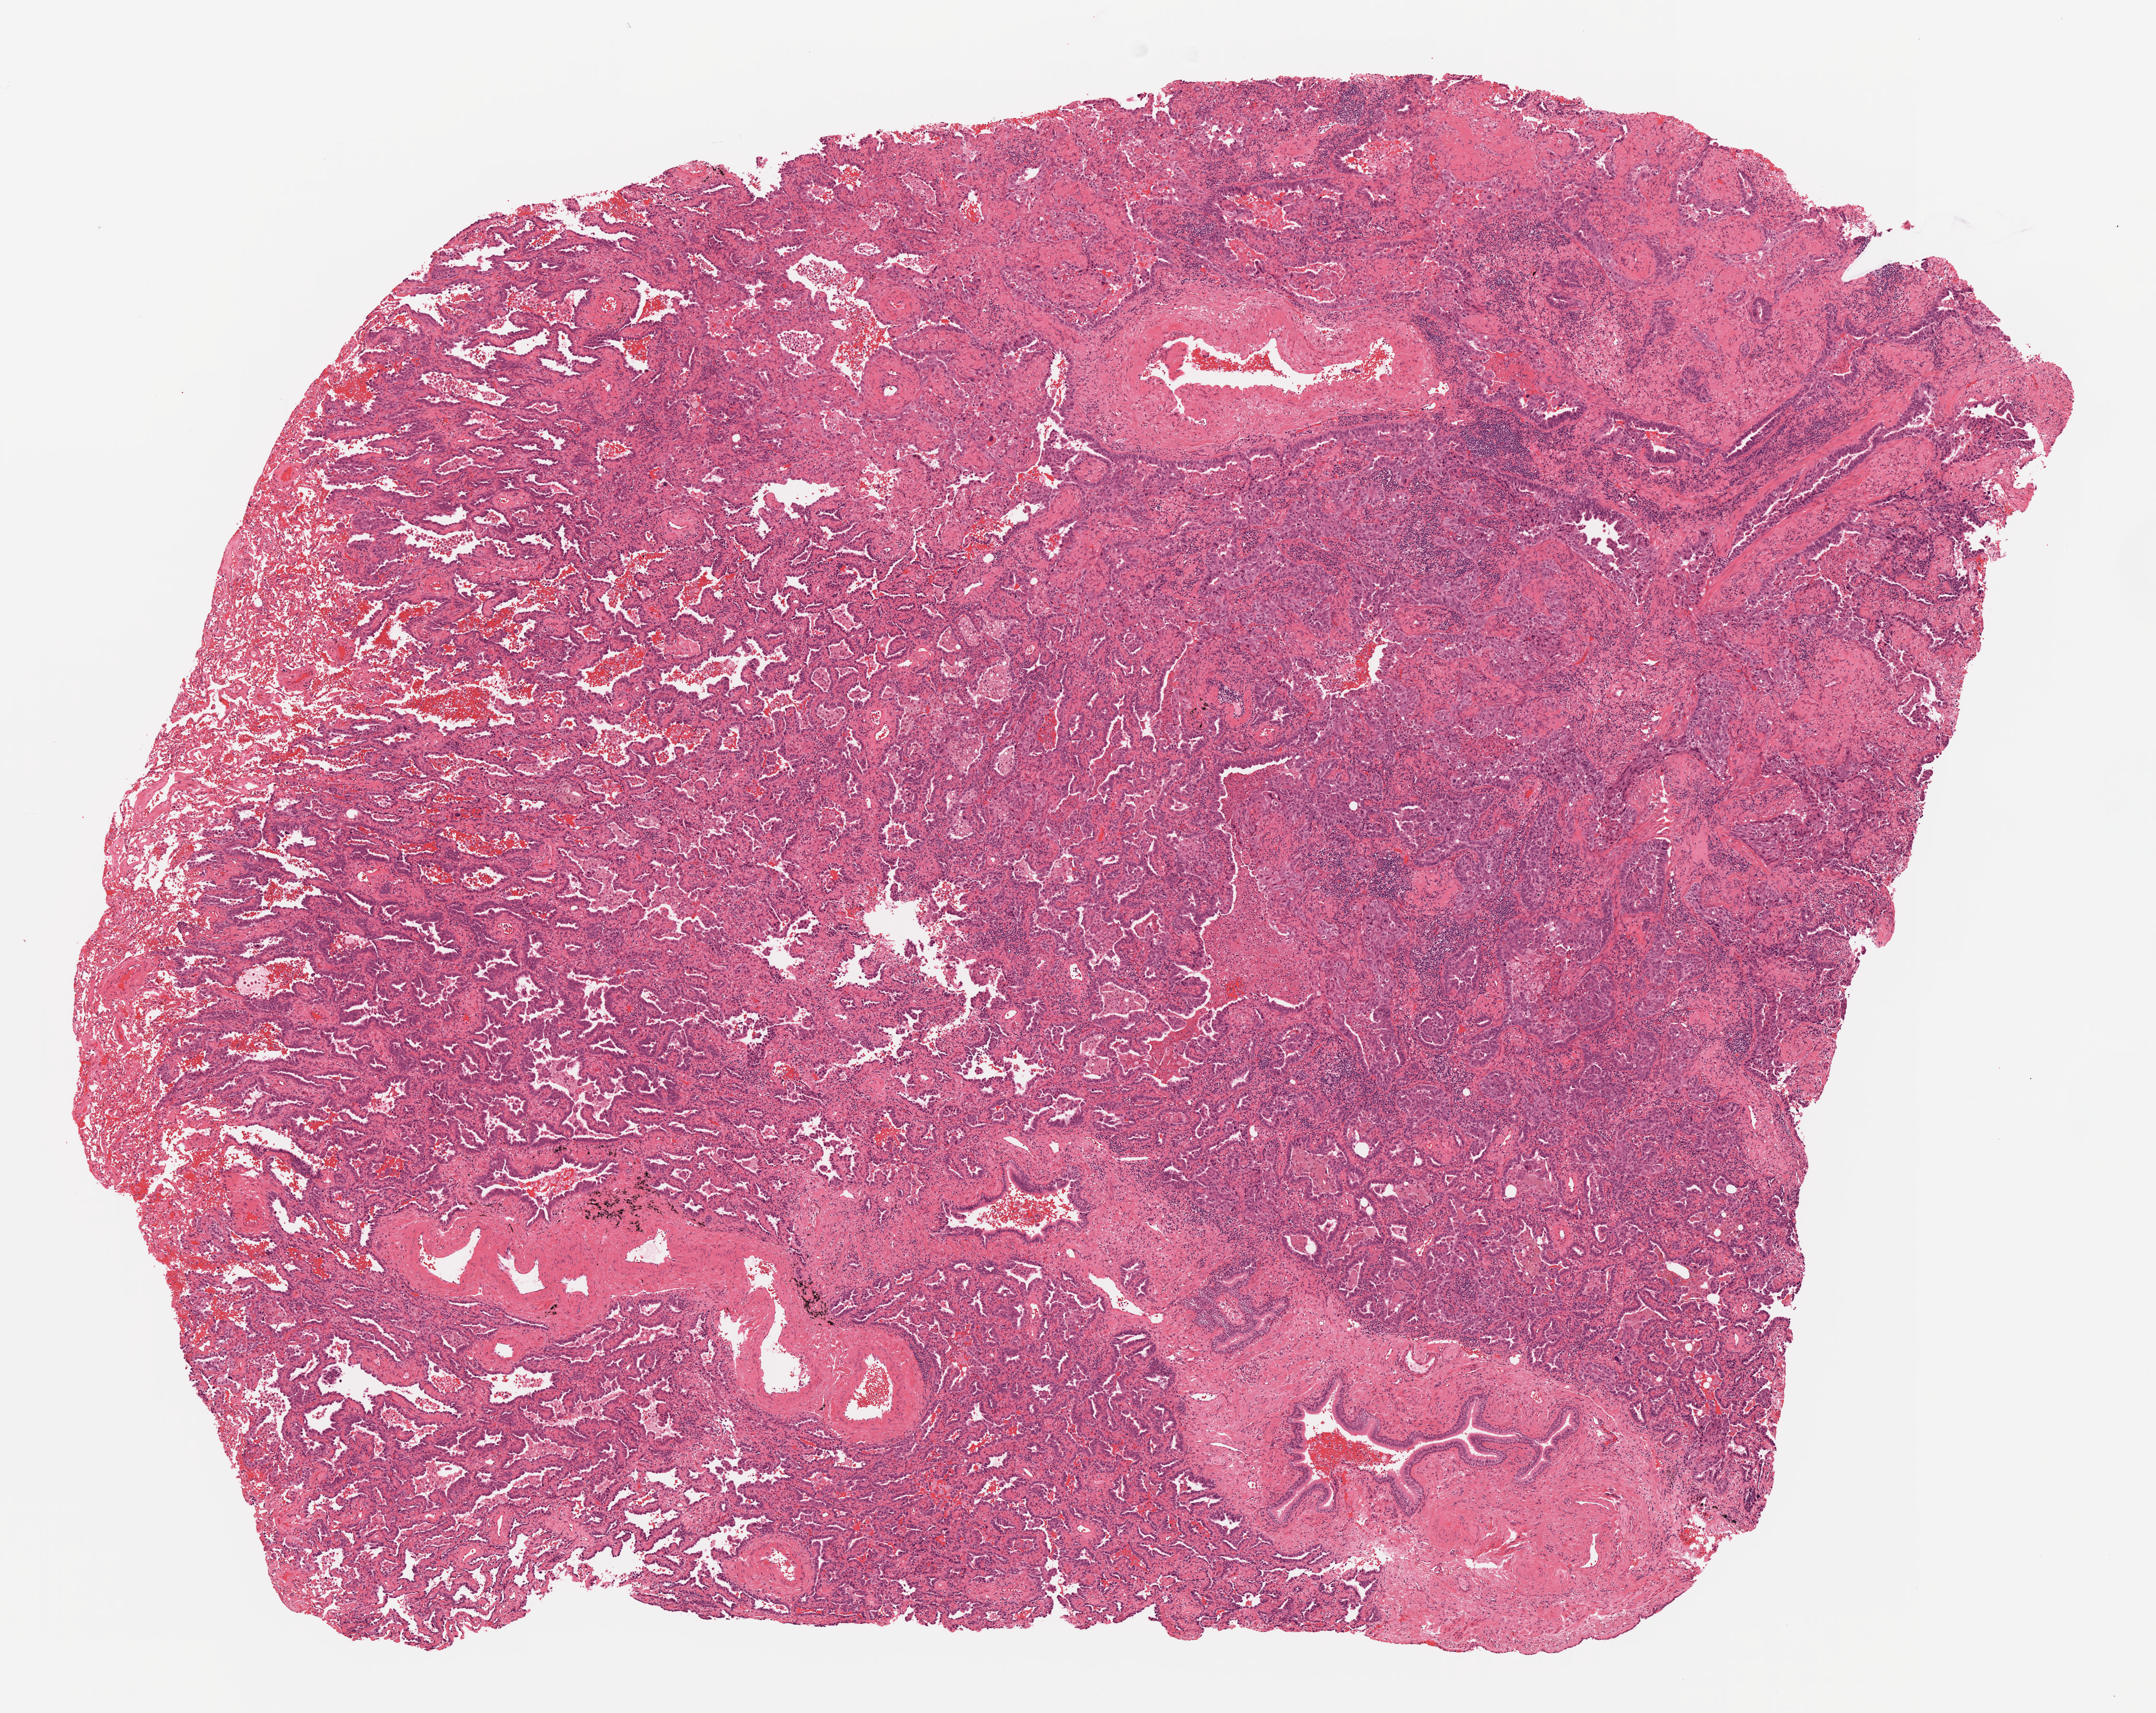
Digitized H&E-stained tissue section (whole slide), shown as a low-resolution overview of the whole scanned area (about 9.0 x 7.2 mm), formalin-fixed paraffin-embedded (FFPE) diagnostic section, primary tumour sample from the lung. Patient sex: female.
Pathologic diagnosis: Bronchiolo-alveolar carcinoma, non-mucinous (upper lobe, lung).